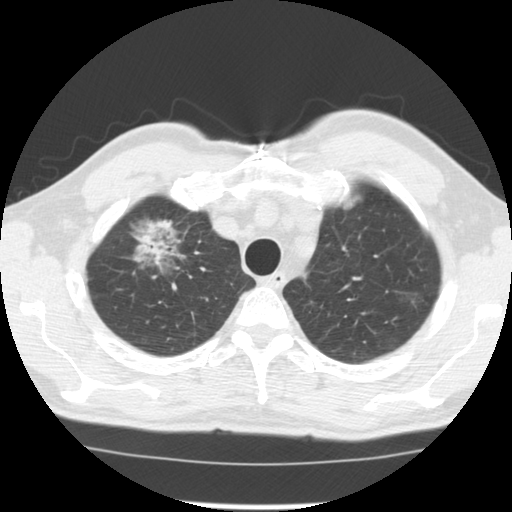
Low-dose screening chest CT, one axial slice. Reconstruction kernel STANDARD. 120 kVp. Lung window (W 1500 / L -600 HU). 512 × 512 image matrix, field of view 340 × 340 mm.
Annotated regions visible in this slice (manually delineated by an expert):
- lesion 1 (tumor, upper lobe of right lung): bounding box (x1, y1, x2, y2) in pixels: (141, 228, 171, 261)